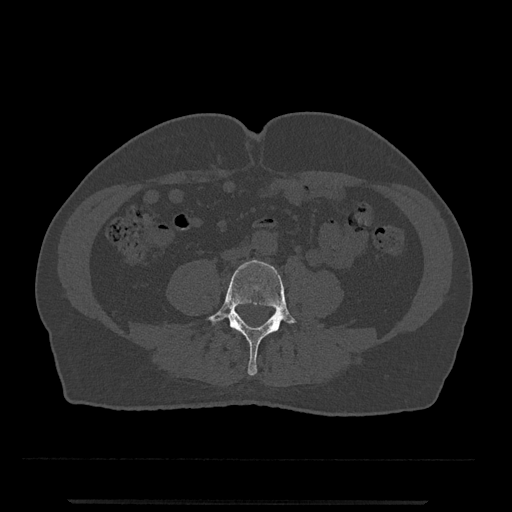
CT including the spine, one axial slice. Position 138 of 797 along the scan axis. Reconstruction kernel Br40s/3. 120 kVp. Bone window (W 1800 / L 400 HU). 0.5 mm slice thickness. 512 × 512 image matrix. Patient: male, 63 years. From the clinical record (not read from this slice): primary cancer: prostate.
Structures marked on this image (semi-automatically segmented with operator editing):
- L4 vertebra: bounding box (x1, y1, x2, y2) in pixels: (206, 260, 296, 375)